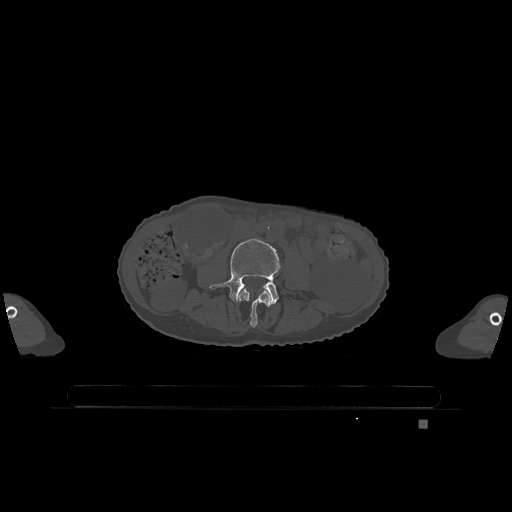
CT including the spine, one axial slice; bone window (W 1800 / L 400 HU); 0.5 mm slice thickness; 512 × 512 image matrix. Female patient, age 74 years. From the clinical record (not read from this slice): primary cancer: lung.
Annotated regions visible in this slice (semi-automatically segmented with operator editing):
- L3 vertebra: bounding box <238,289,271,327> (left, top, right, bottom; pixels)
- L4 vertebra: <210,239,281,305>